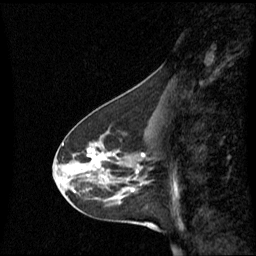
Breast MRI (dynamic contrast-enhanced), one sagittal slice; slice 28 of 60 in the series (ordered by position); dynamic contrast-enhanced series, image 2 of 3 at this slice position (ordered by acquisition); 1.5 T; TE 4.2 ms, TR 8.4 ms; 2.2 mm slice thickness; 256 × 256 image matrix, field of view 240 × 240 mm. Female patient, age 45 years. Case-level facts recorded for this patient, not image findings: setting: breast cancer imaged before/during neoadjuvant chemotherapy; receptor status: HR-positive, HER2-negative.
Structures marked on this image (semi-automatically segmented with operator editing):
- analysis volume of interest (the breast-tissue region the enhancement analysis was run in; not a lesion): box from (x=60, y=126) to (x=149, y=215) px
- tumour enhancement mask (voxels above the 70 % enhancement threshold inside the analysis volume of interest): (x=87, y=148)–(x=144, y=191)